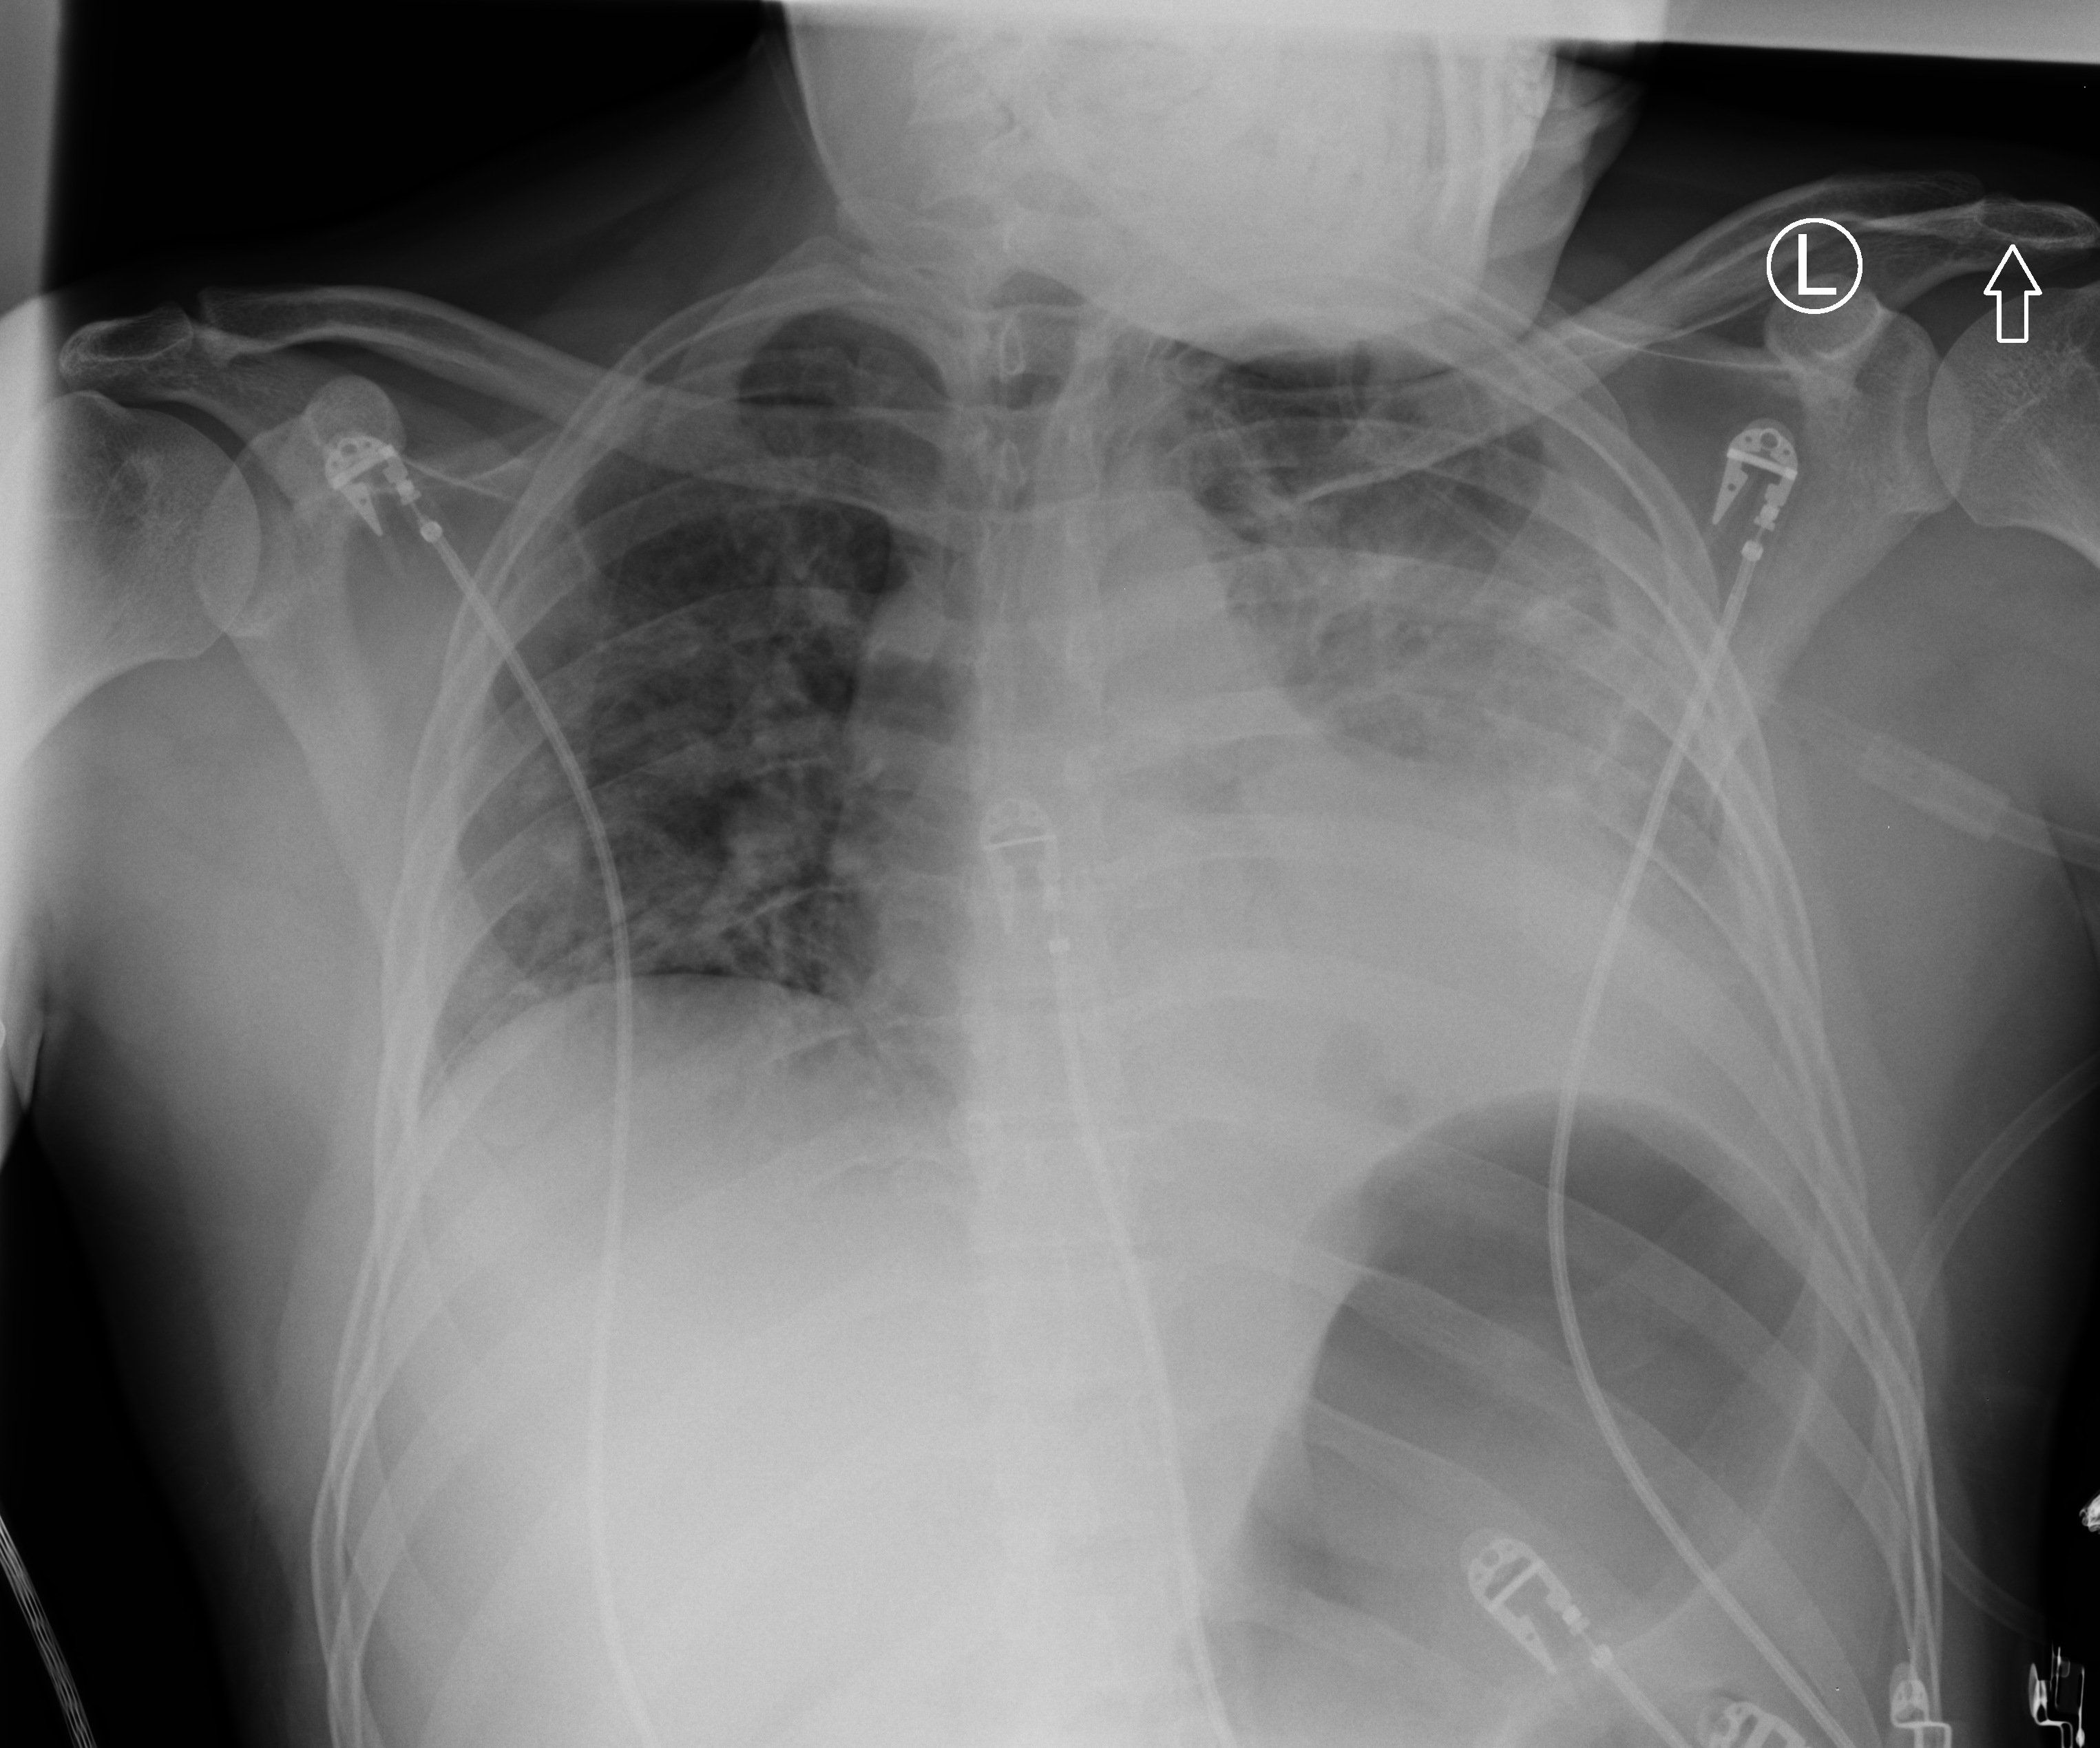
Chest X-ray (portable), anteroposterior (AP) projection. Patient hospitalised with COVID-19; male, aged 18–59 years.
Admission-level facts for this patient (not findings on this image; timing relative to this image not recorded): mechanically ventilated during this hospital stay: yes.